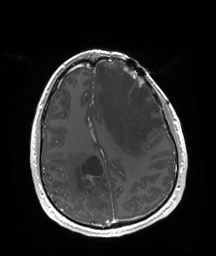
Brain MRI from a brain-tumour surgery series, one axial slice; slice 61 of 192 in the series (ordered by position); T1-weighted post-contrast; 1 mm slice thickness; 216 × 256 image matrix, field of view 219 × 260 mm. Case-level facts recorded for this patient, not image findings: tumour location: Left Frontal.
Annotated regions visible in this slice (outlined manually by an expert reader):
- tumour: bounding box [x1, y1, x2, y2] px = [123, 66, 144, 87]